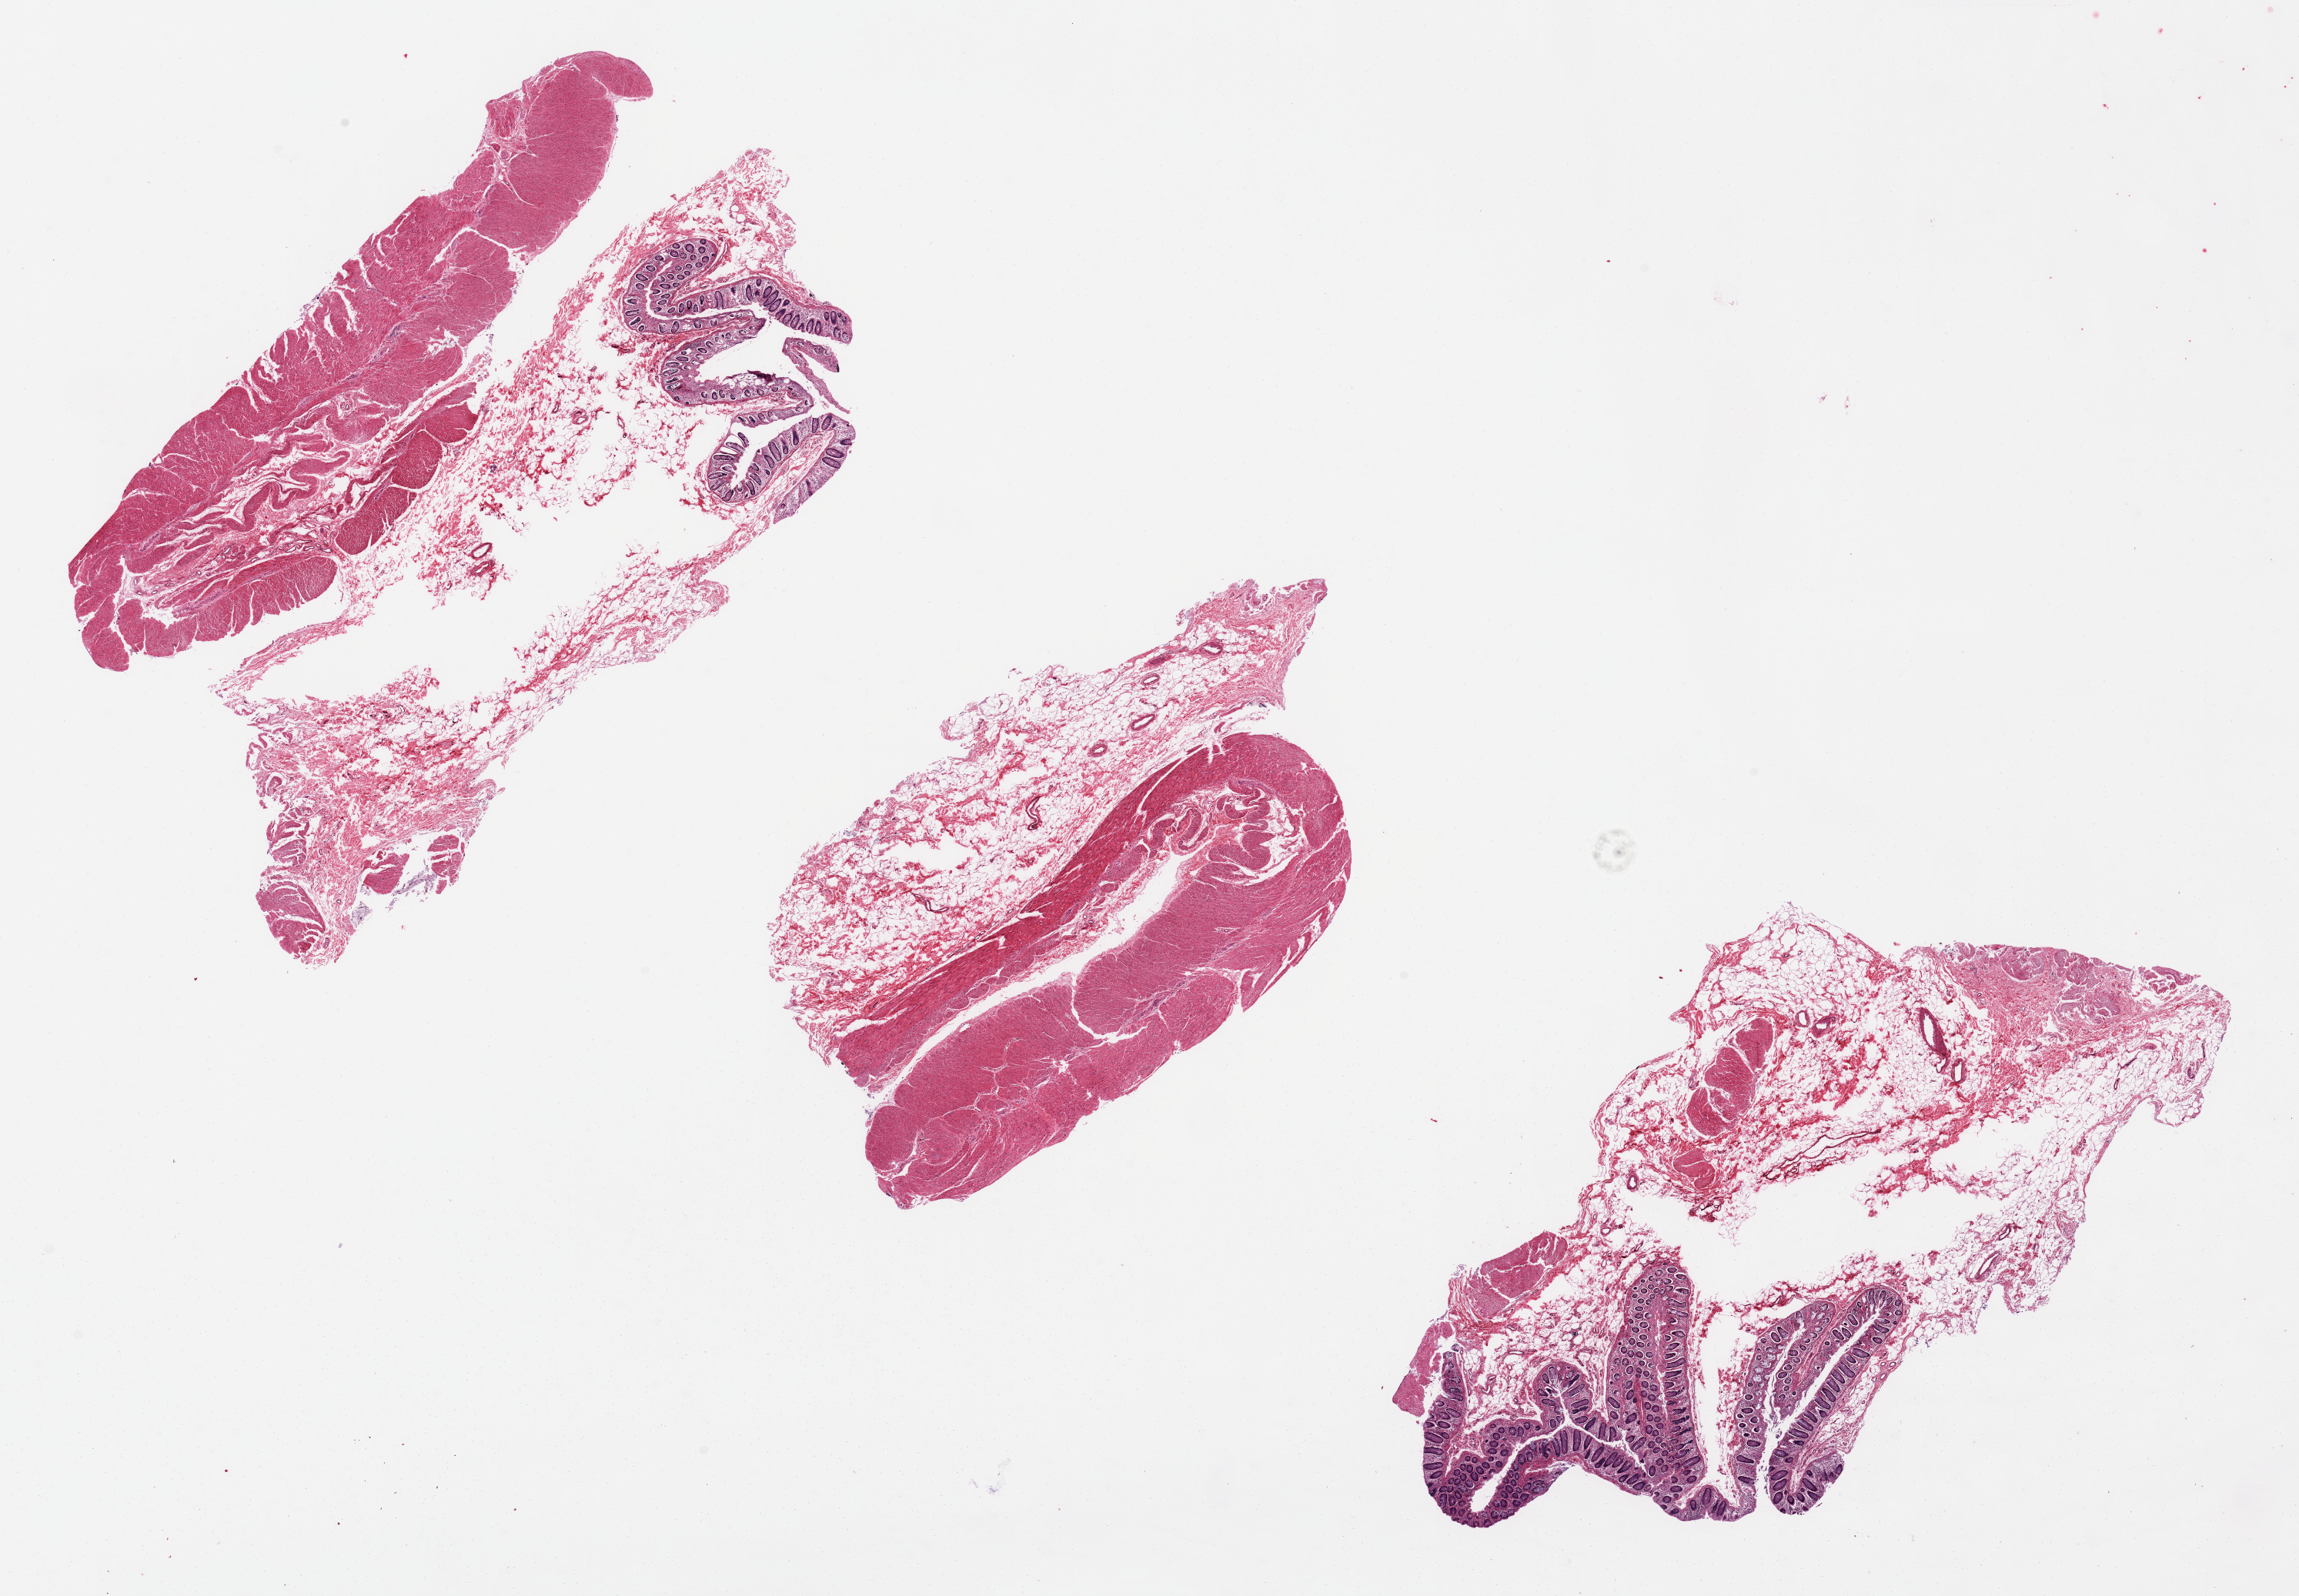
Hematoxylin and eosin (H&E) whole-slide image, shown as a low-resolution overview of the whole scanned area (about 23.6 x 16.4 mm, acquisition: 20x scan); PAXgene-fixed, paraffin-embedded tissue; target tissue: transverse colon; donor tissue sample. Donor sex: male.
- reviewer comment on this tissue sample: 2 of 3 with mucosa. 9.6x5.8mm